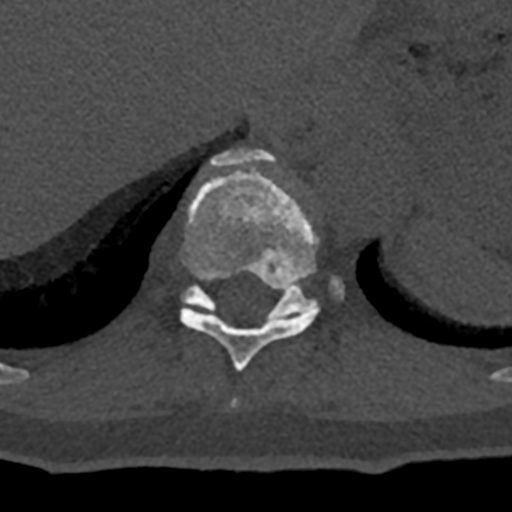
CT including the spine, one axial slice. Position 588 of 797 along the scan axis. Reconstruction kernel Br40s/3. 120 kVp. Bone window (W 1800 / L 400 HU). 0.5 mm slice thickness. 512 × 512 image matrix, field of view 160 × 160 mm. Patient: male, 74 years. Case-level facts recorded for this patient, not image findings: primary cancer: renal.
Structures marked on this image (semi-automatically segmented with operator editing):
- T10 vertebra: bounding box (x1, y1, x2, y2) in pixels: (180, 148, 319, 372)
- T11 vertebra: (182, 275, 344, 319)